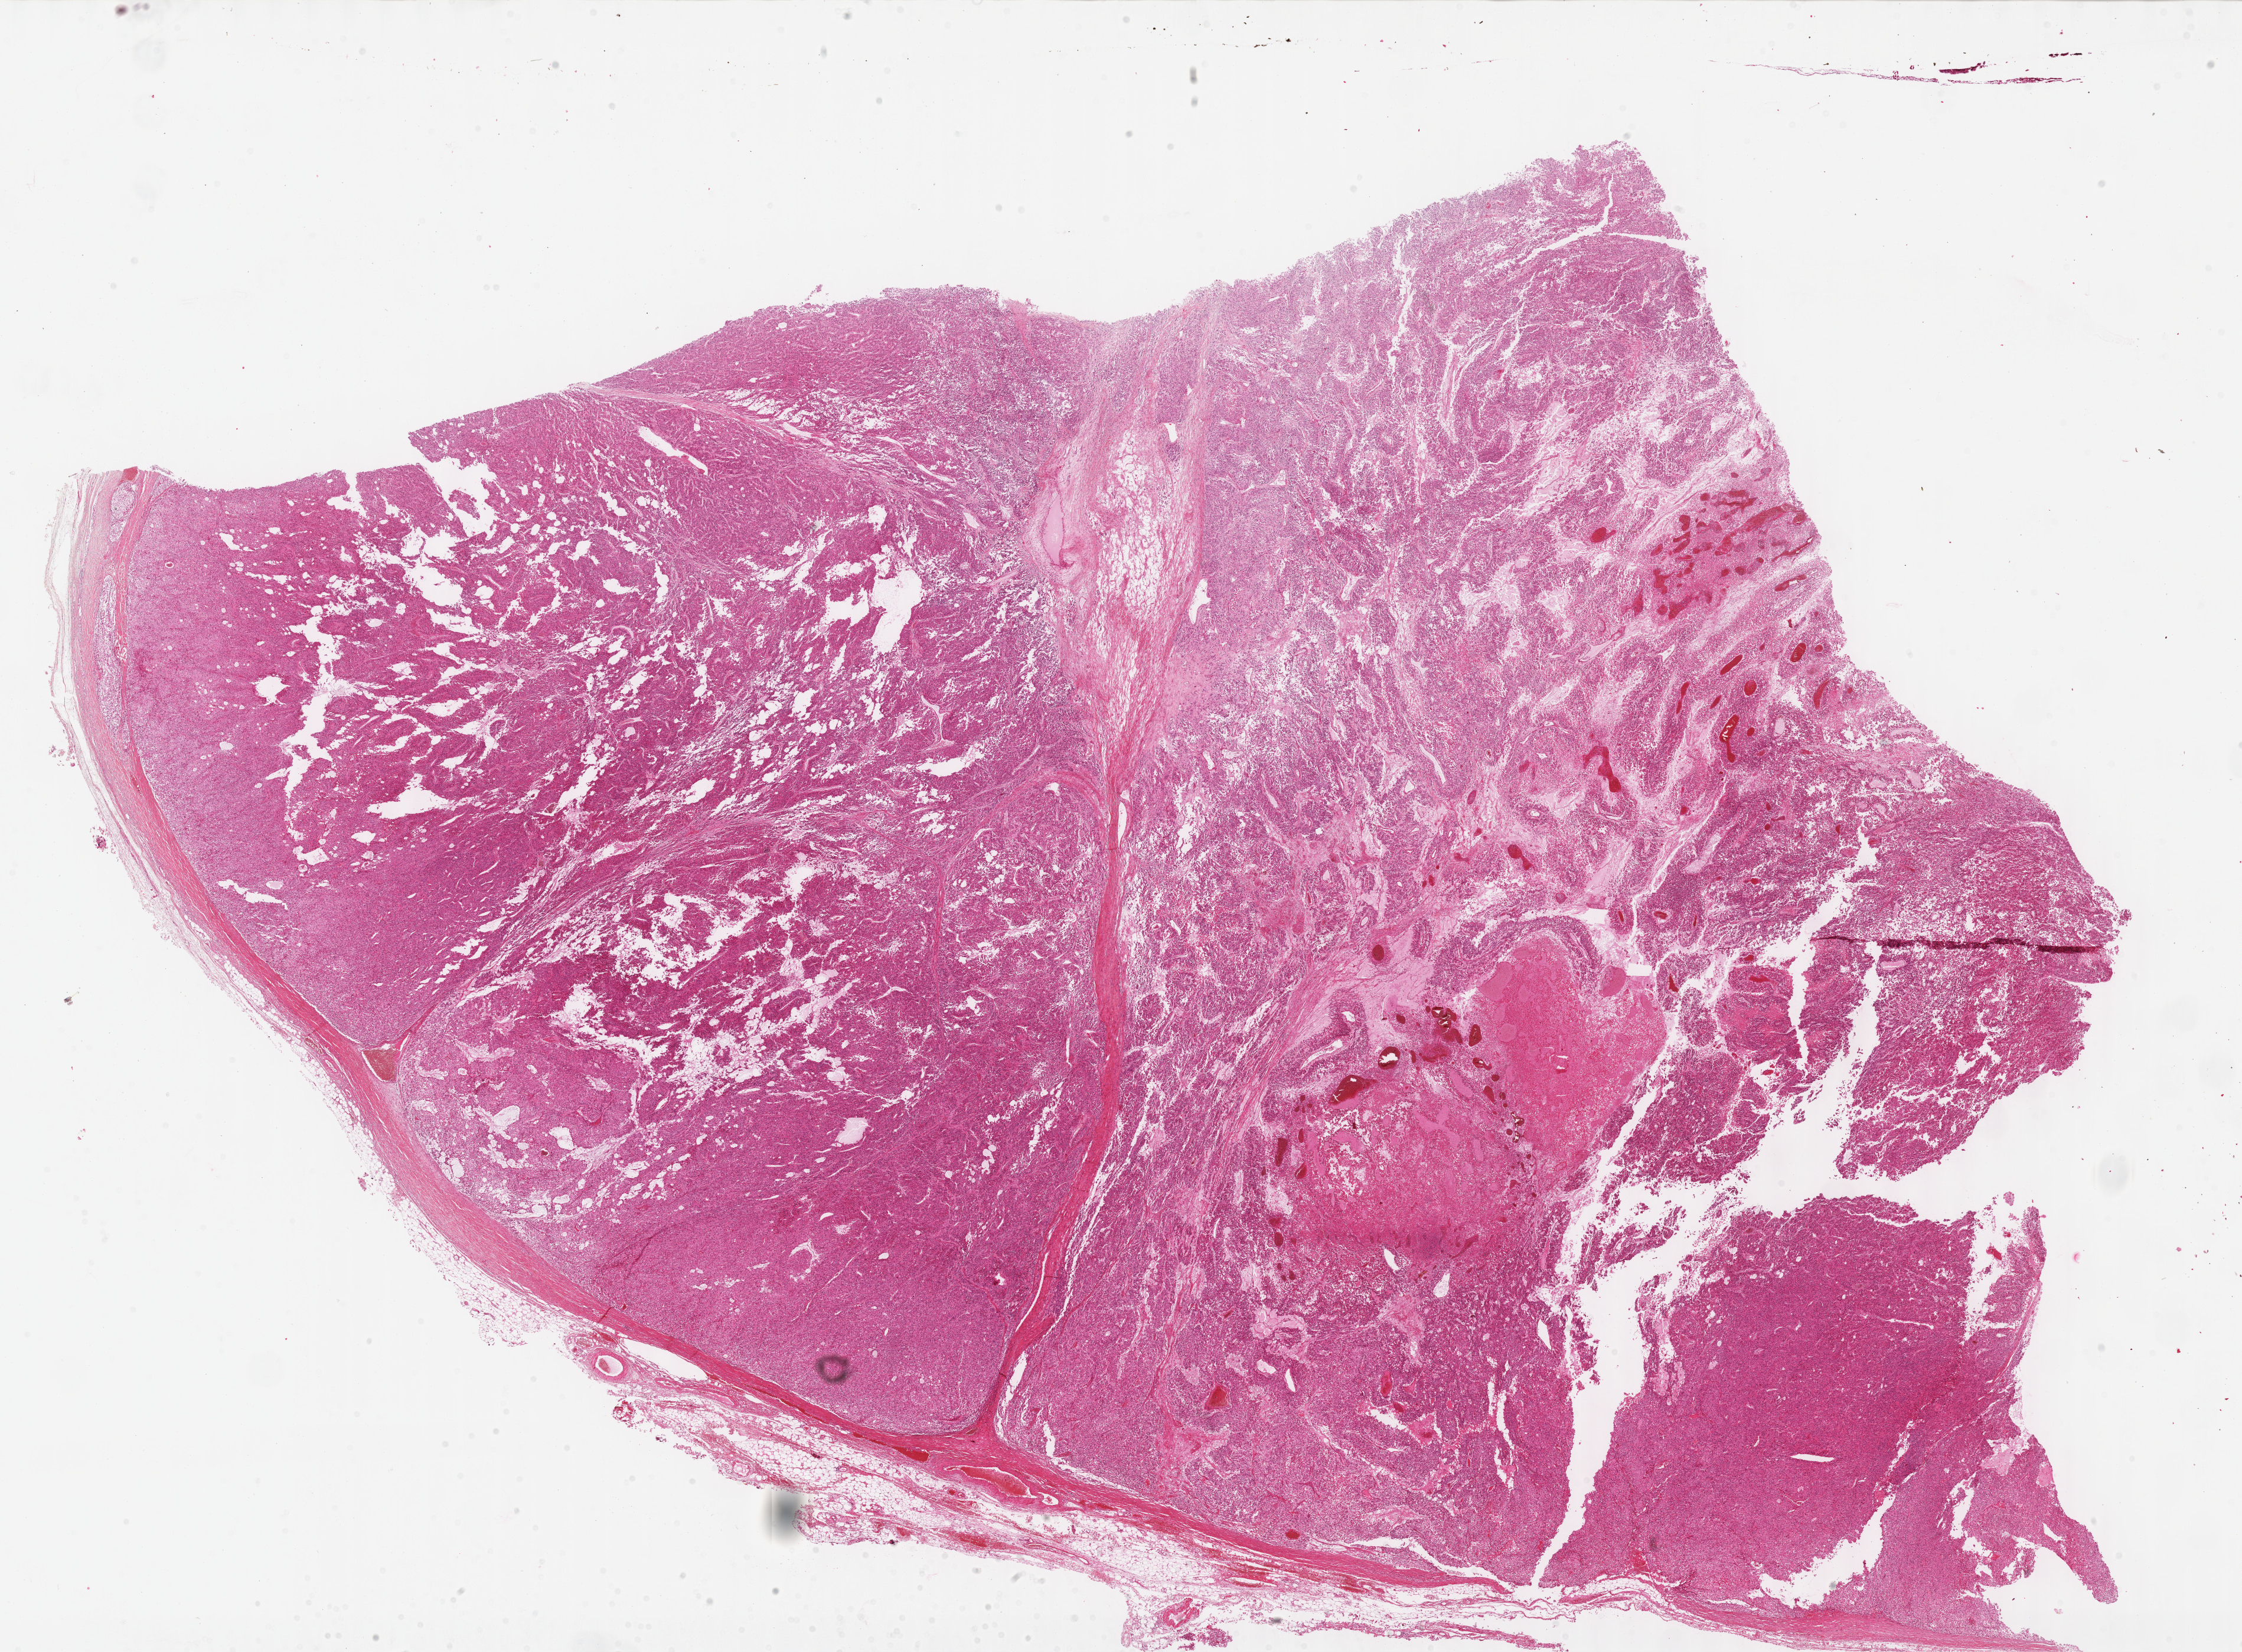
Digitized H&E-stained tissue section (whole slide), shown as a low-resolution overview of the whole scanned area (about 30.7 x 22.6 mm). FFPE section. Primary tumour sample from the adrenal cortex. Female, age 61 years at initial diagnosis.
* lymph nodes positive (case pathology): 0 of 19 examined
* histologic diagnosis: Adrenal cortical carcinoma (cortex of adrenal gland)